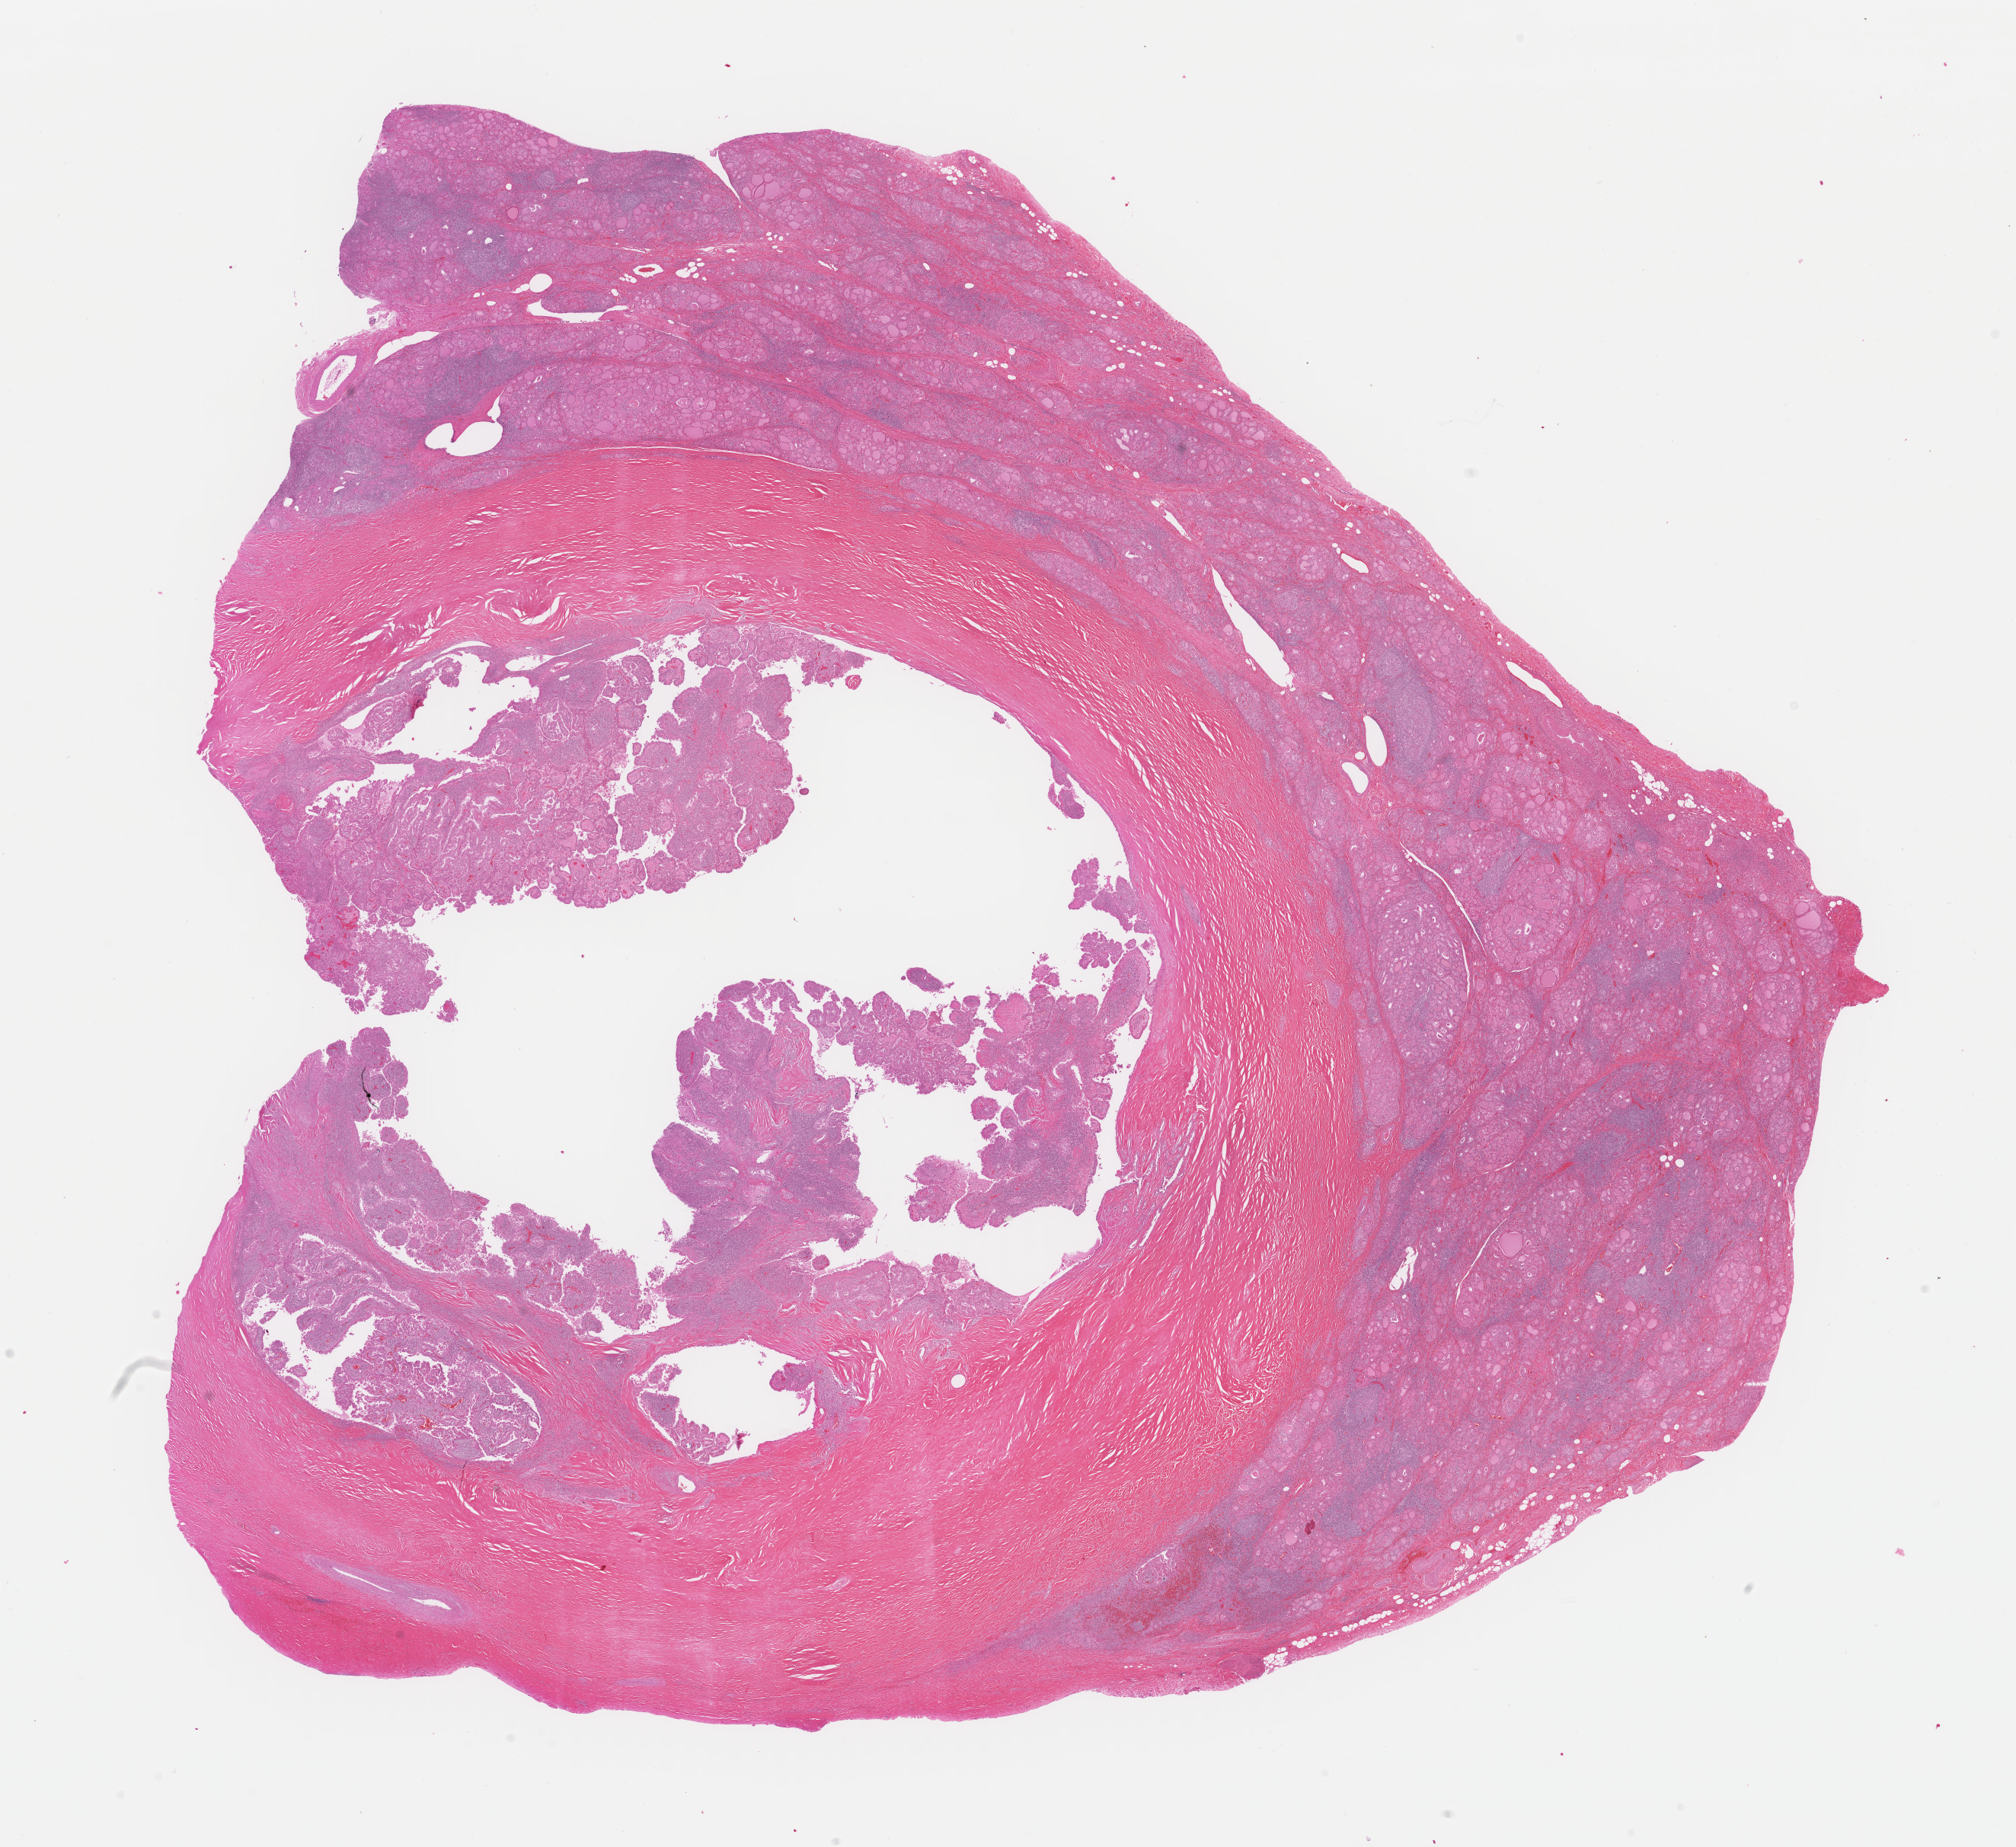
H&E whole-slide image, whole scanned area (about 20.9 x 19.1 mm) shown as a low-resolution overview. FFPE section. Primary tumour sample from the thyroid. Patient: female, age at initial diagnosis 31 years.
Diagnosis: Papillary adenocarcinoma, NOS (thyroid gland). Lymph nodes positive (case pathology): 0 of 1 examined. AJCC pathologic stage: I (6th edition).